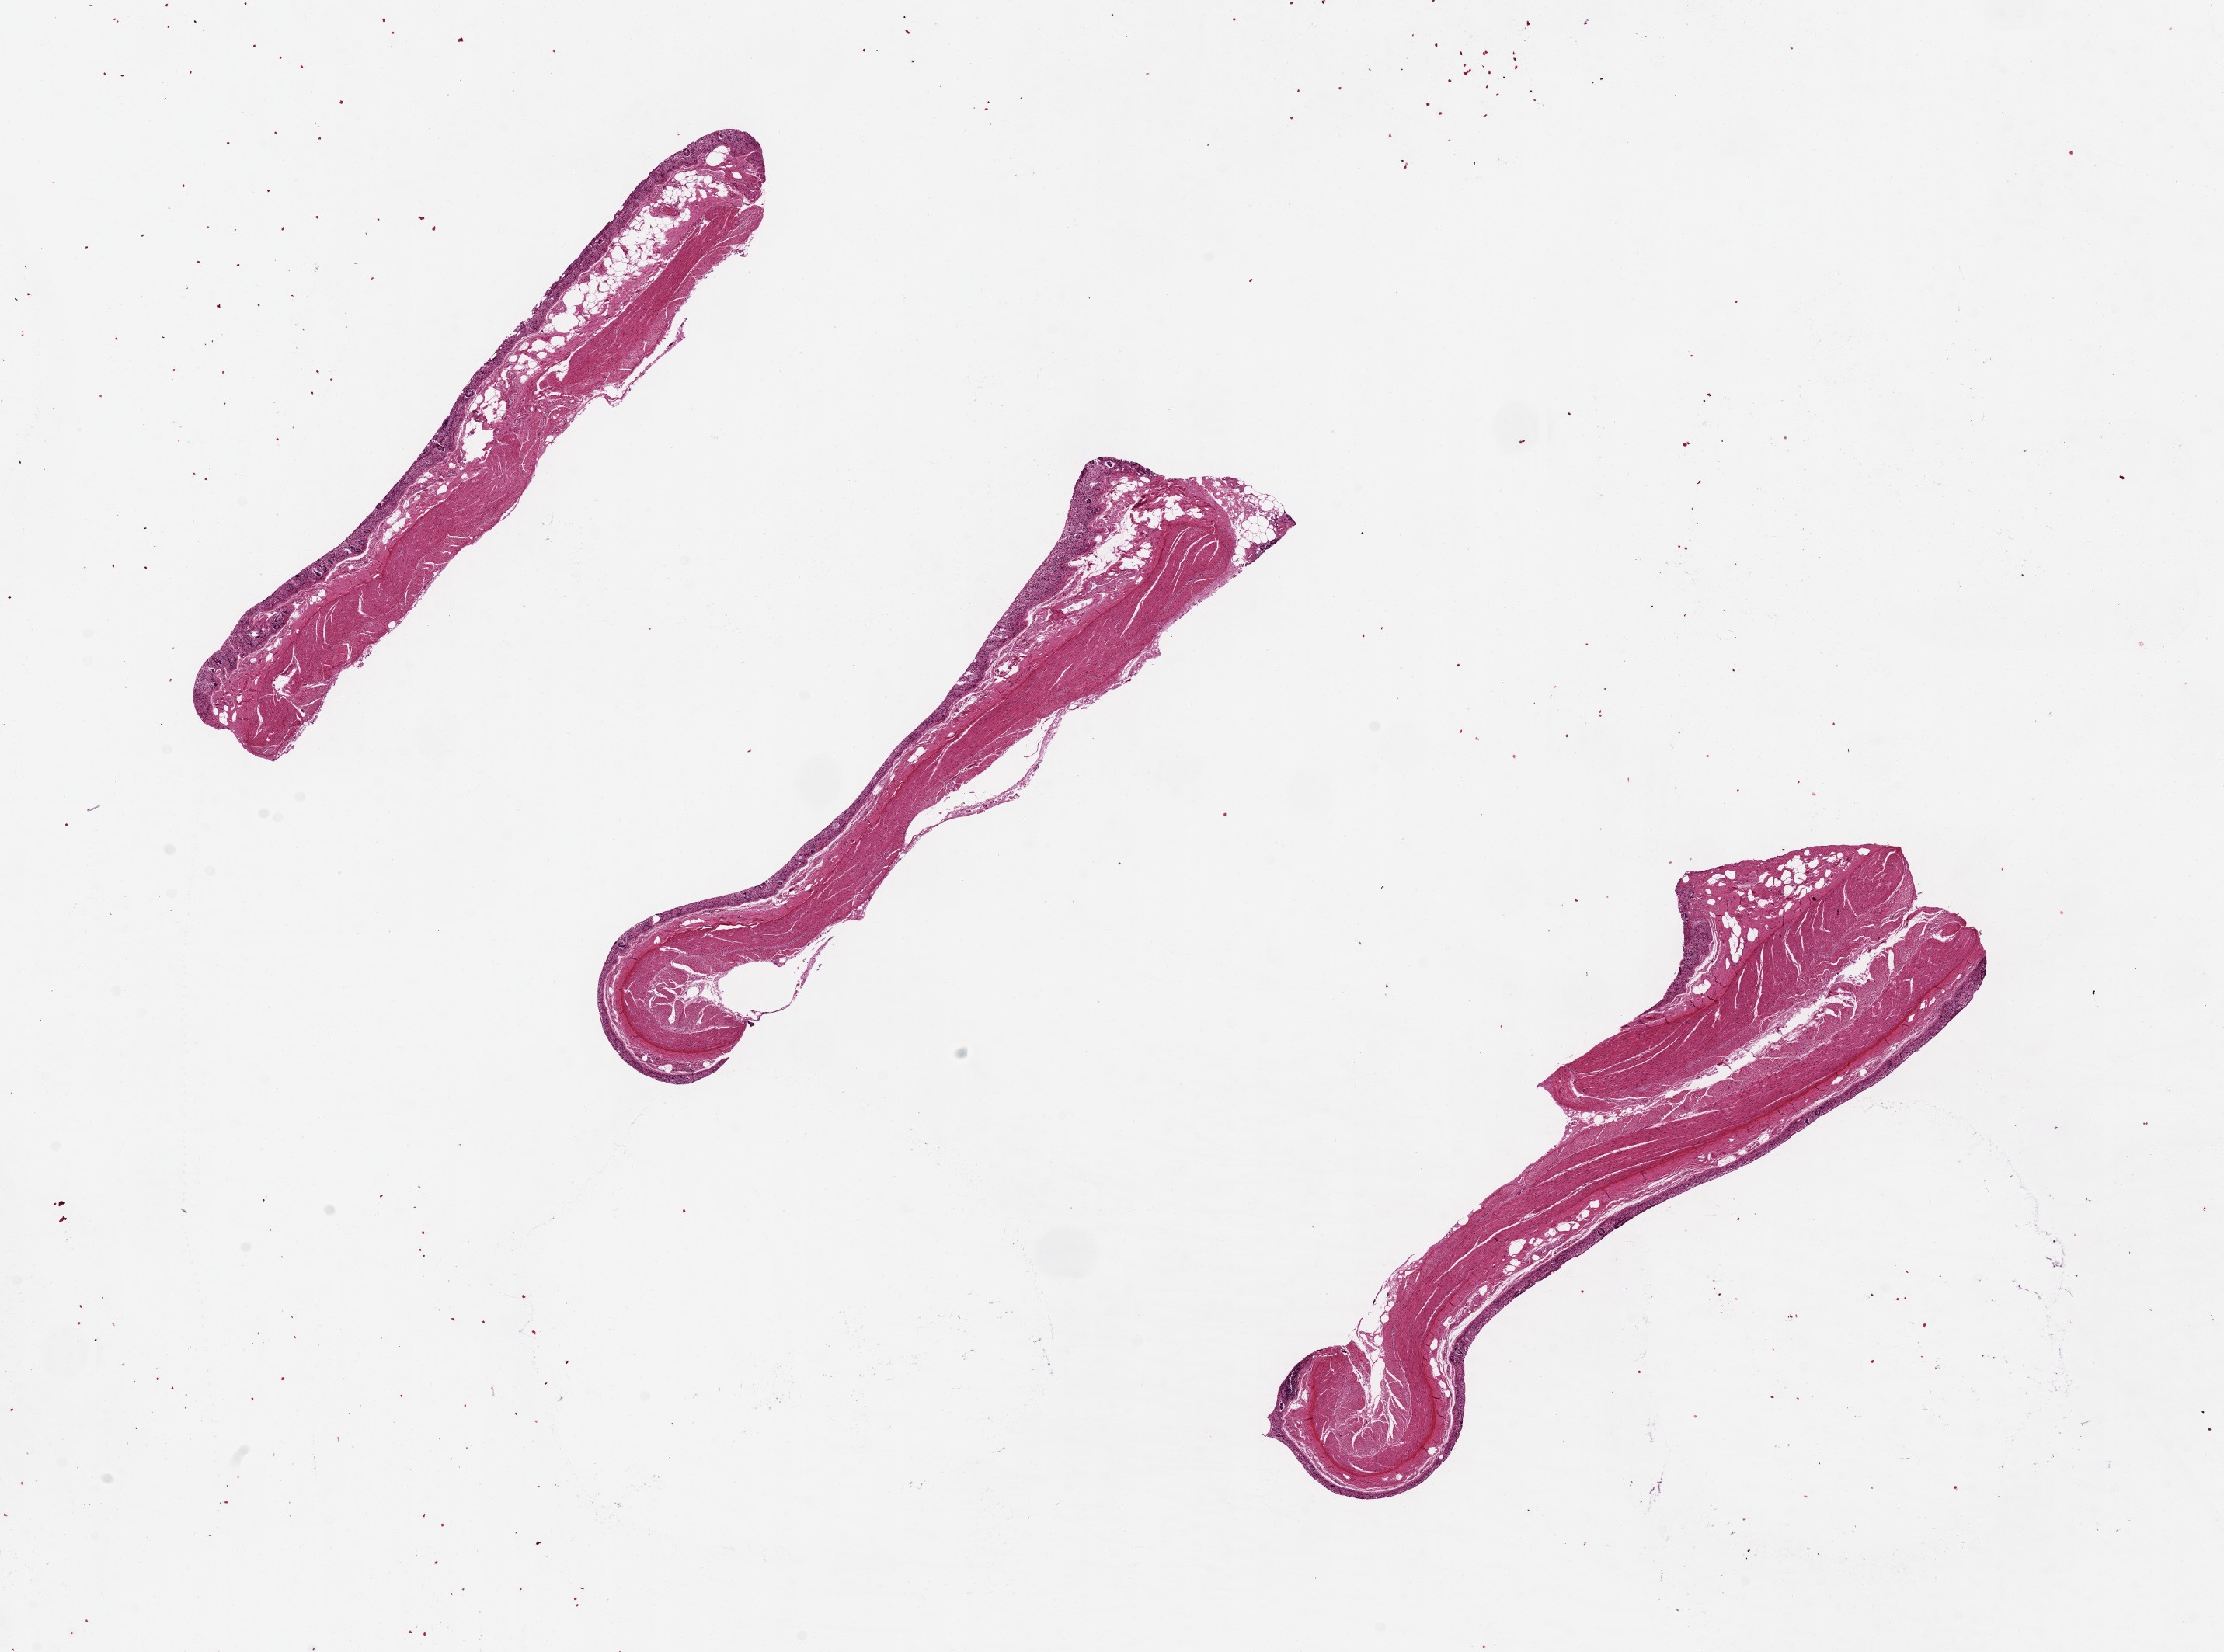
Whole-slide image, haematoxylin and eosin stain, brightfield — shown as a low-resolution overview of the whole scanned area (about 22.6 x 16.8 mm, from a 20x scan), PAXgene-fixed, paraffin-embedded tissue, target tissue: transverse colon, tissue donor sample. Donor: male.
Reviewer comment on this tissue sample: Severely autolyzed mucosa.